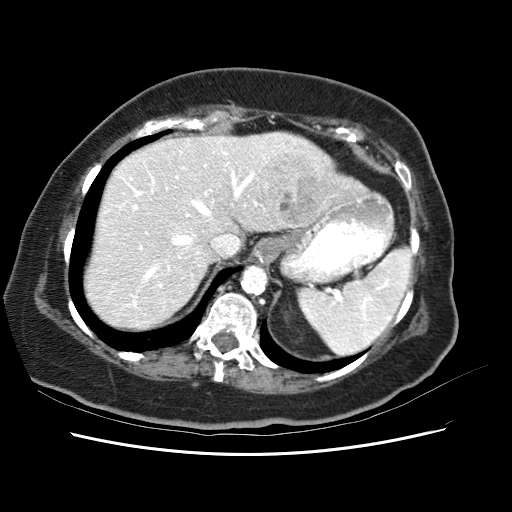
Contrast-enhanced abdominal CT (liver protocol), one axial slice; position 48 of 62 along the scan axis; 120 kVp; soft-tissue window (W 400 / L 40 HU); 512 × 512 image matrix. From the clinical record (not read from this slice): diagnosis: hepatocellular carcinoma (patient treated with transarterial chemoembolisation; whether this scan precedes or follows treatment is not stated here); TNM stage (as recorded): Stage-I; Child-Pugh class: B; tumour nodularity: uninodular.
Annotated regions visible in this slice (semi-automatically segmented with operator editing):
- liver parenchyma outside the tumour (the mass and vessels are separate outlines, so this box may not span the whole liver): box from (x=97, y=134) to (x=336, y=316) px
- mass: (x=258, y=148)–(x=332, y=219)
- liver vessels: (x=124, y=153)–(x=261, y=299)